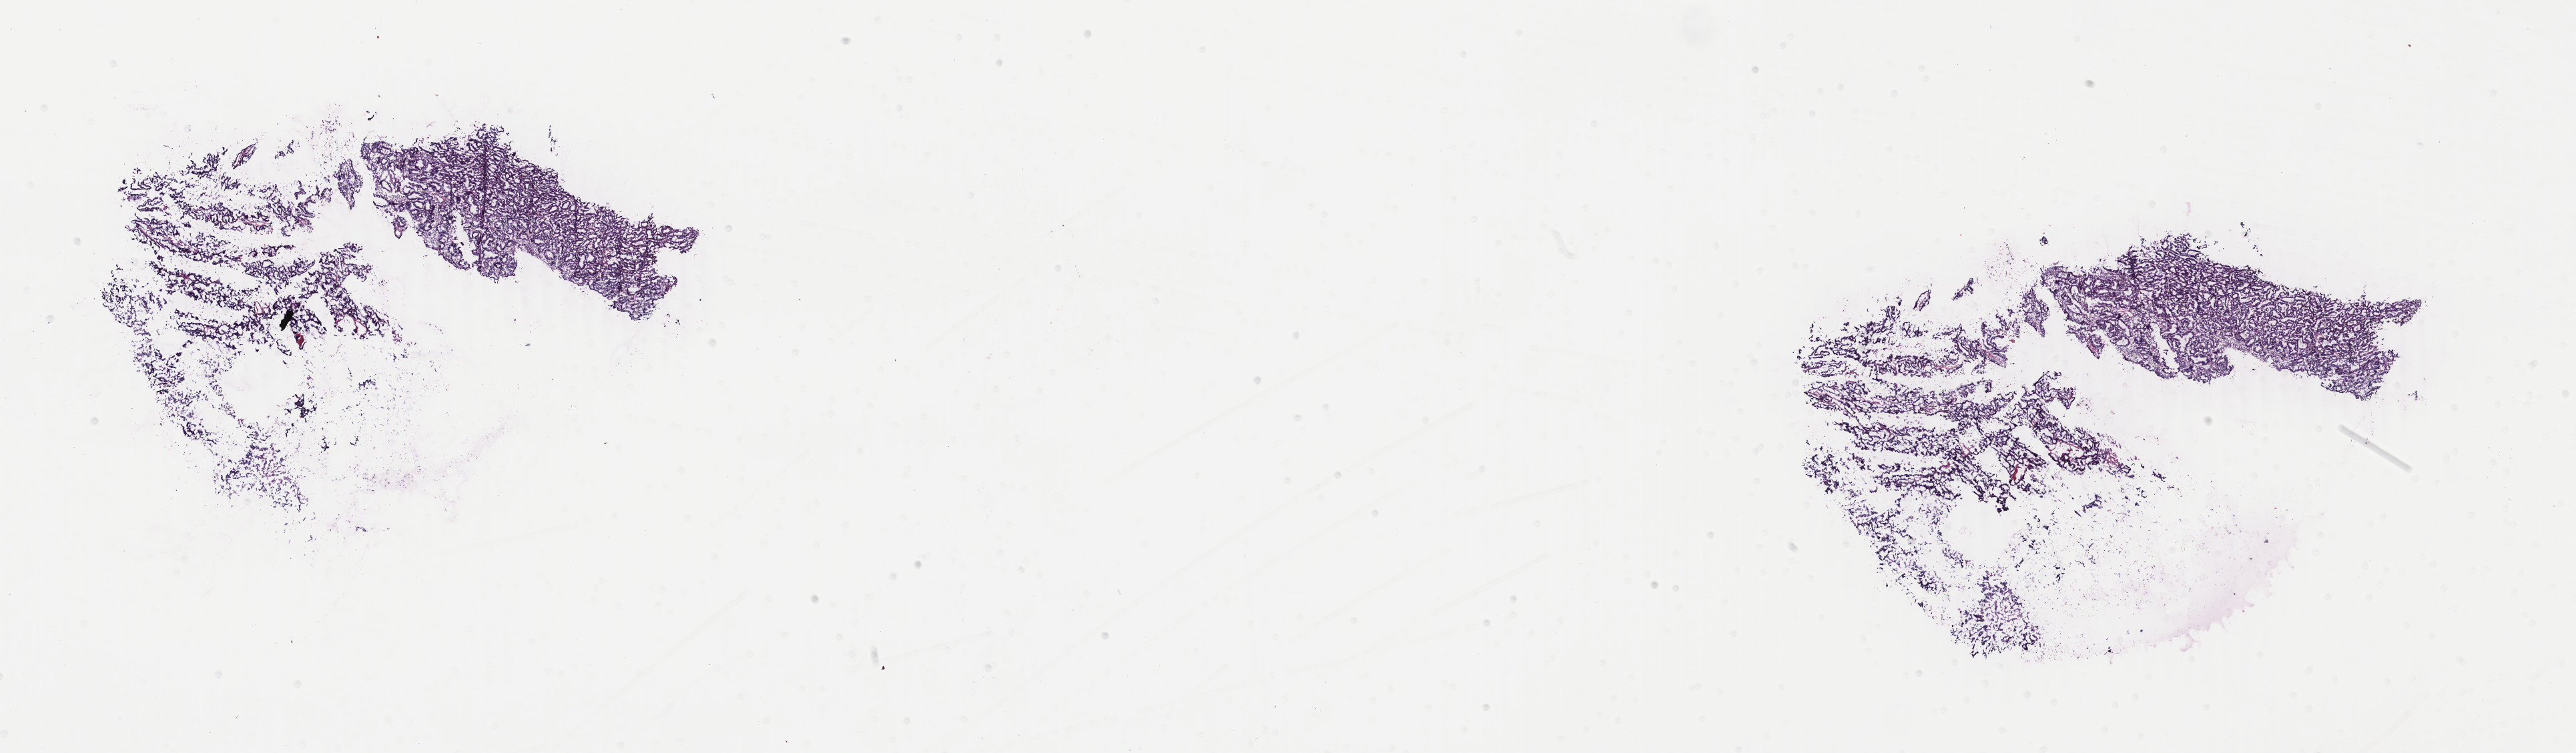
Hematoxylin and eosin (H&E) stained whole-slide image, shown as a low-resolution overview of the whole scanned area (about 30.7 x 9.0 mm), frozen section, uterus, primary tumour sample. Female patient; age at initial diagnosis 64 years. Histologic grade: G1 (well differentiated). Pathologist review of this section (percent, as recorded): tumour cells 100%, tumour nuclei 85%, normal cells 0%, stromal cells 0%, necrosis 0%. Inflammatory infiltration, as recorded: lymphocyte infiltration 0%, monocyte infiltration 0%, neutrophil infiltration 0%.
Histologic diagnosis: Endometrioid adenocarcinoma, NOS (endometrium). FIGO stage: IA.